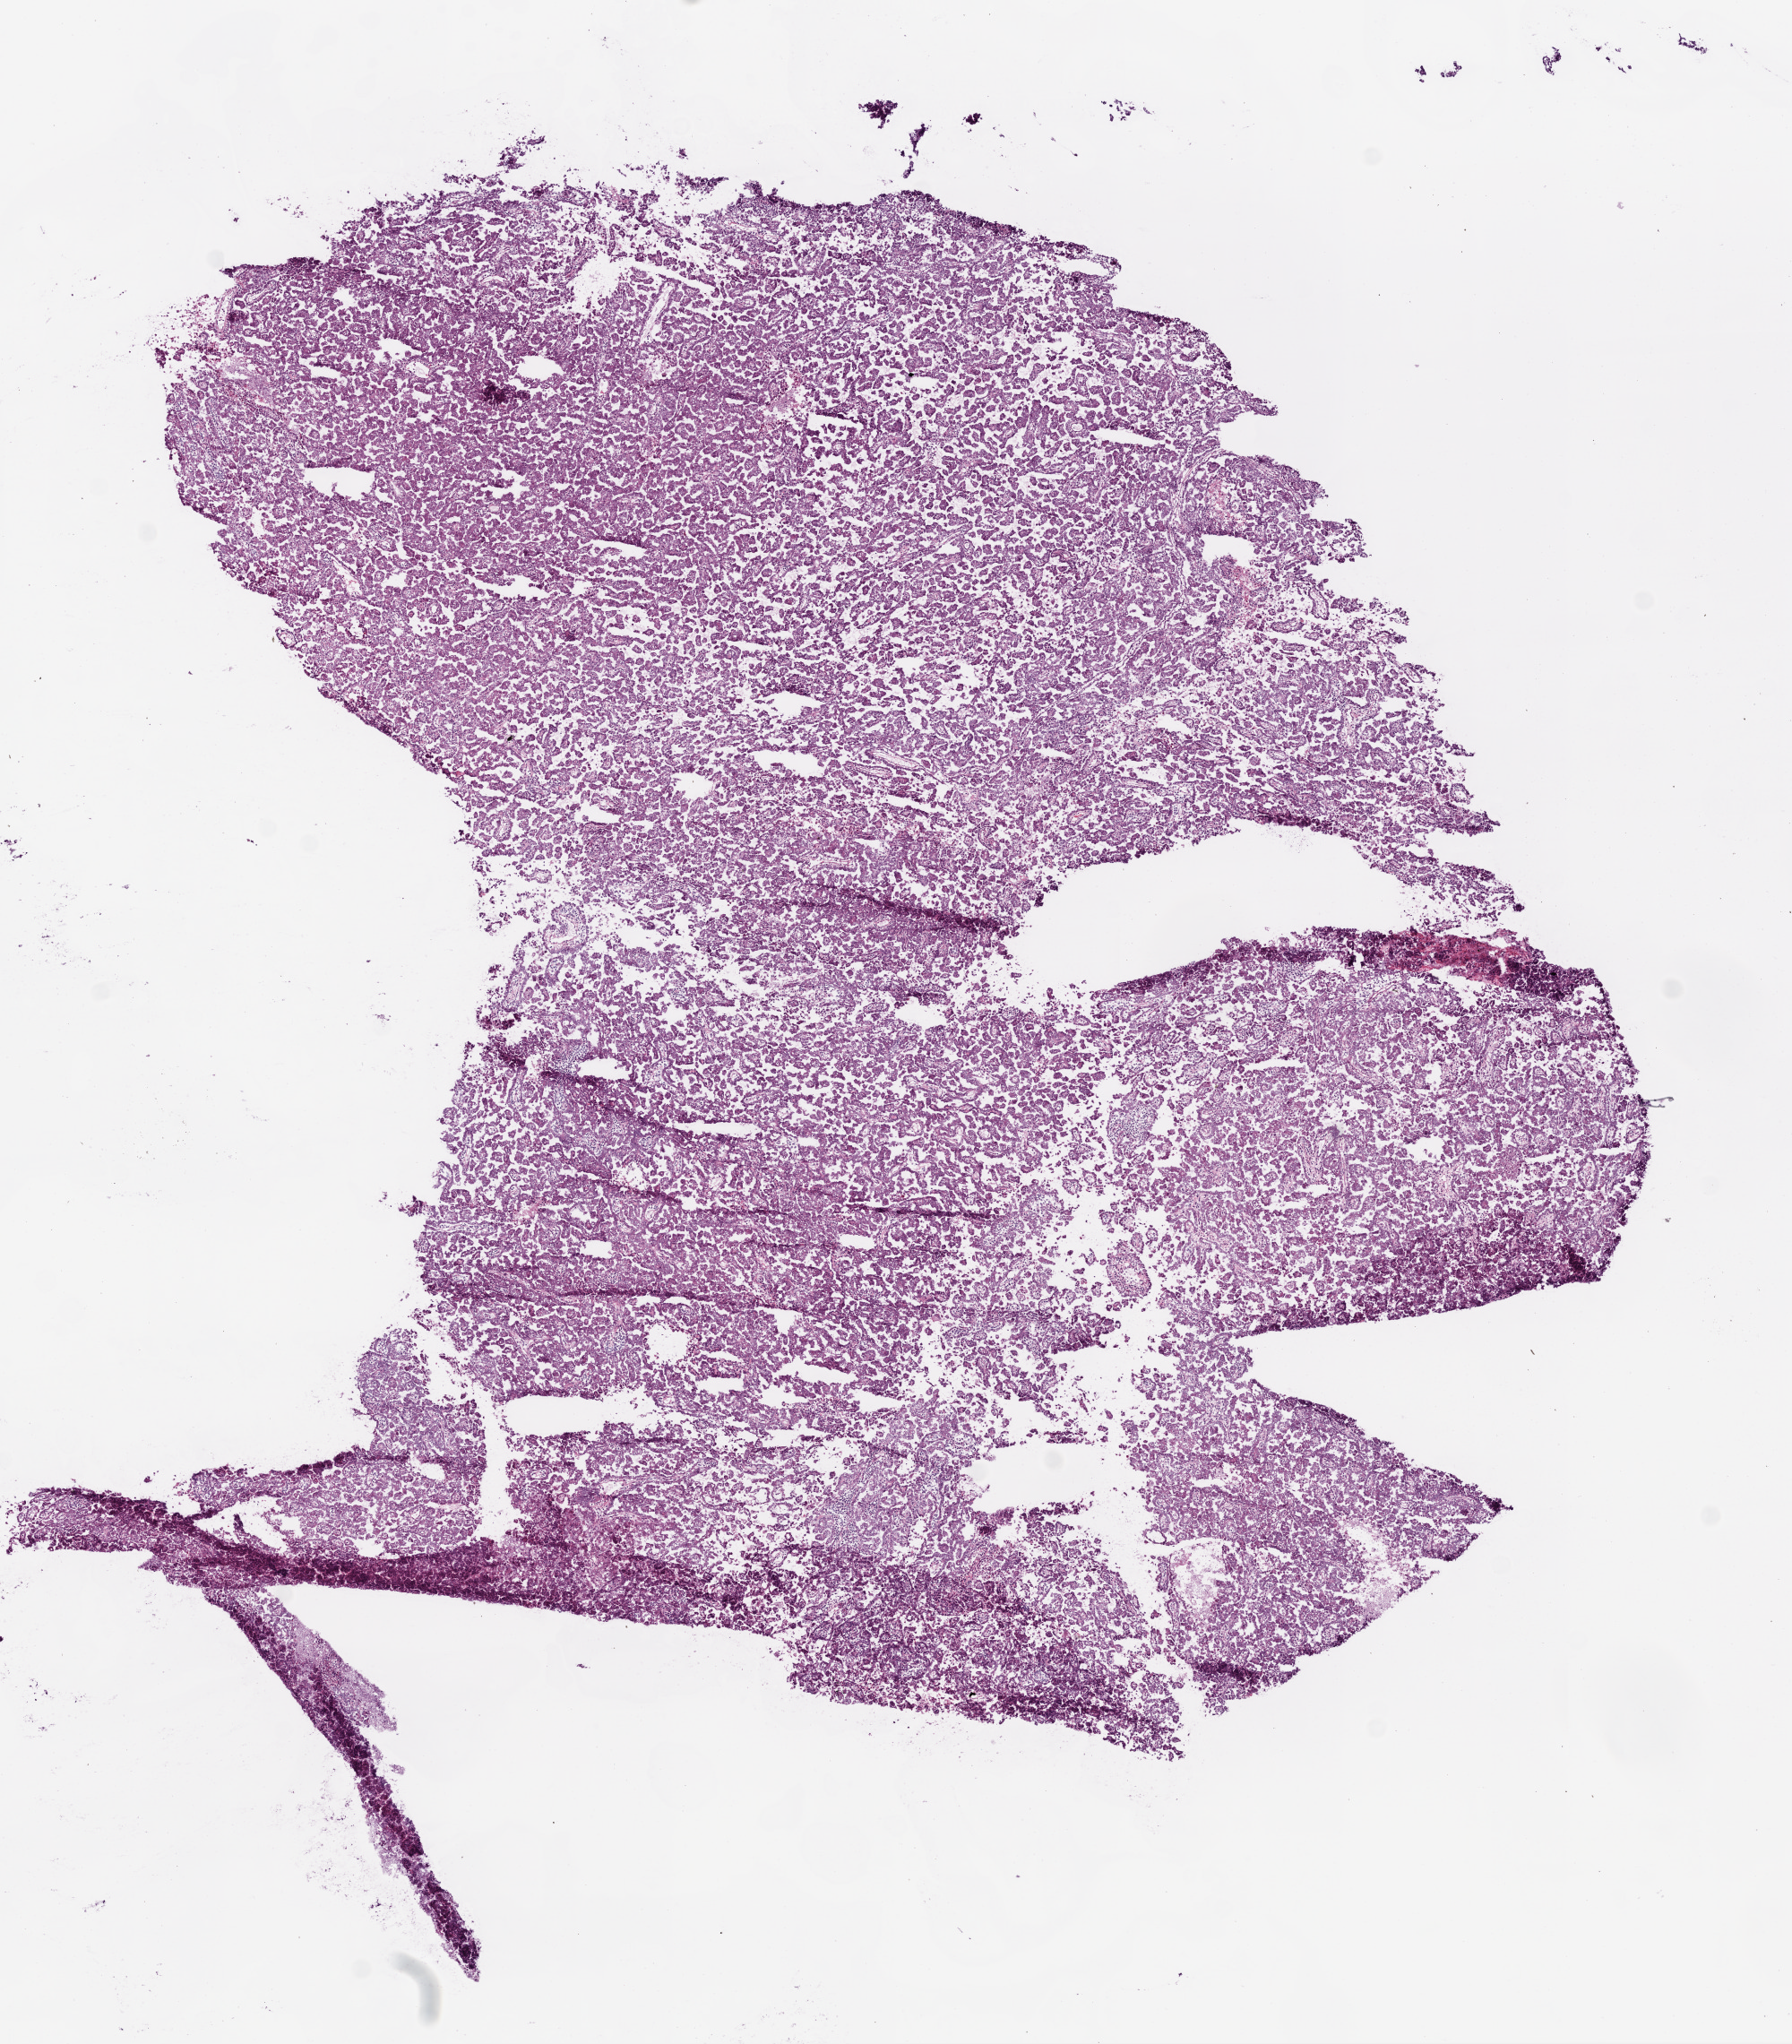
Digitized H&E-stained tissue section (whole slide), shown as a low-resolution overview of the whole scanned area (about 8.0 x 9.2 mm), frozen section from the top of the tissue portion, primary tumour sample from the kidney. Female, age 75 years at initial diagnosis. Pathologist review of this section (percent, as recorded): tumour cells 80%, tumour nuclei 85%, normal cells 0%, stromal cells 20%, necrosis 0%.
Diagnosis: Papillary adenocarcinoma, NOS.